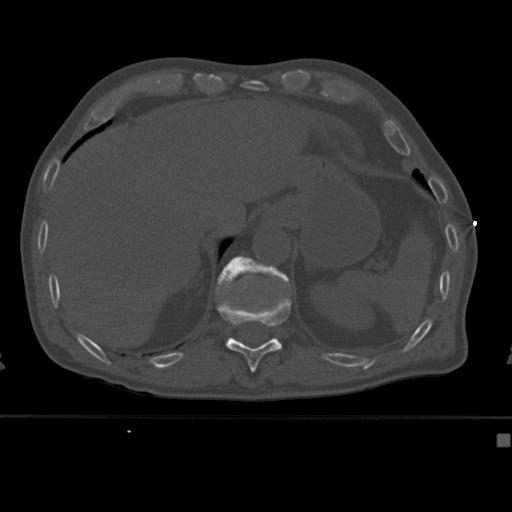
CT including the spine, one axial slice; position 206 of 430 along the scan axis; reconstruction kernel Br40s; bone window (W 1800 / L 400 HU); 1.5 mm slice thickness; 512 × 512 image matrix, field of view 337 × 337 mm. Patient: male, 64 years. From the clinical record (not read from this slice): primary cancer: uterus.
Annotated regions visible in this slice (semi-automatically segmented with operator editing):
- T11 vertebra: bounding box [x1, y1, x2, y2] px = [217, 294, 292, 373]
- T12 vertebra: [216, 256, 288, 294]